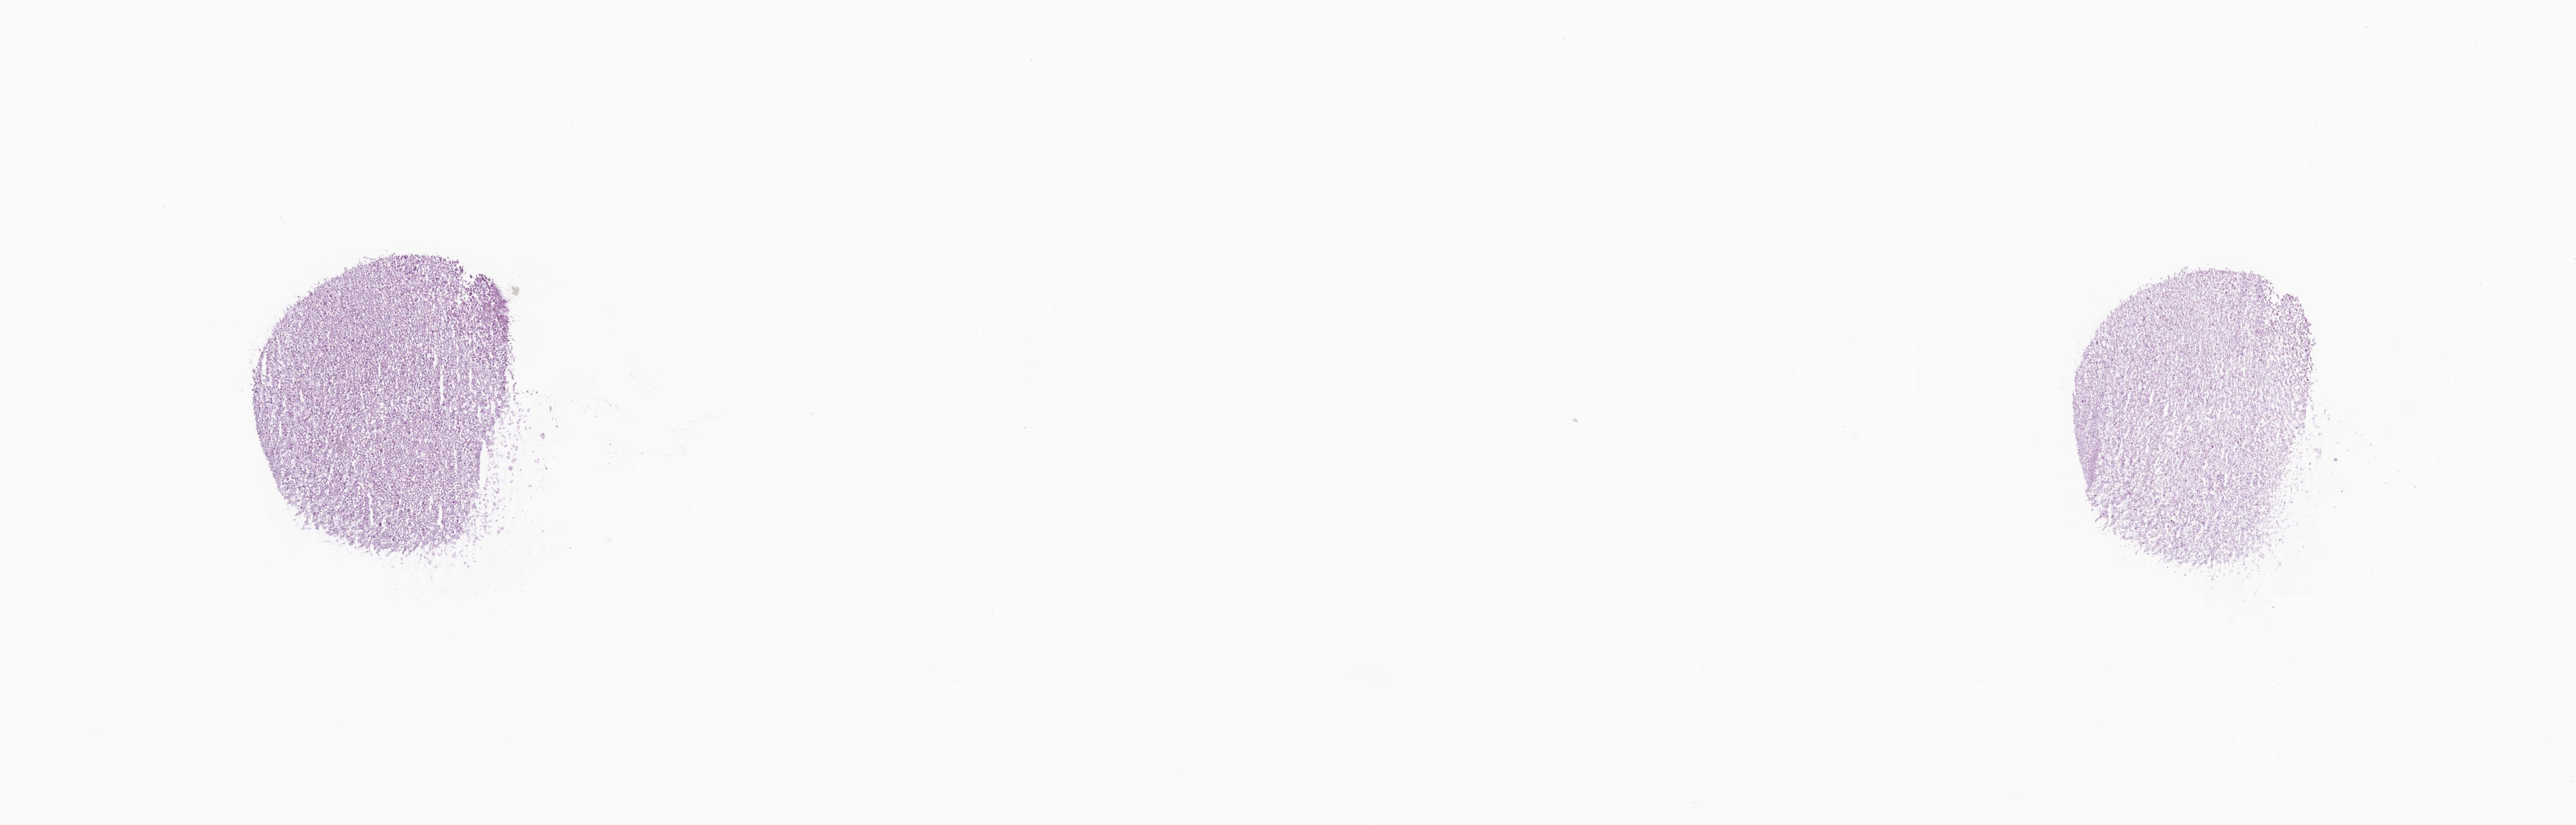
Digitized H&E-stained section — shown as a low-resolution overview of the whole scanned area (about 18.9 x 6.0 mm), frozen section (tissue freezing medium), metastatic tumor tissue. Female patient; age at initial diagnosis 50 years. Slide review estimates, as recorded: tumor cells 95%, tumor nuclei 95%, stromal cells 5%, necrosis 0%, normal cells 0%. Inflammatory infiltration, as recorded: lymphocyte infiltration 0%, monocyte infiltration 0%, neutrophil infiltration 0%.
Section: top of the tissue portion. Patient diagnosis (primary): Adenocarcinoma, metastatic, NOS.